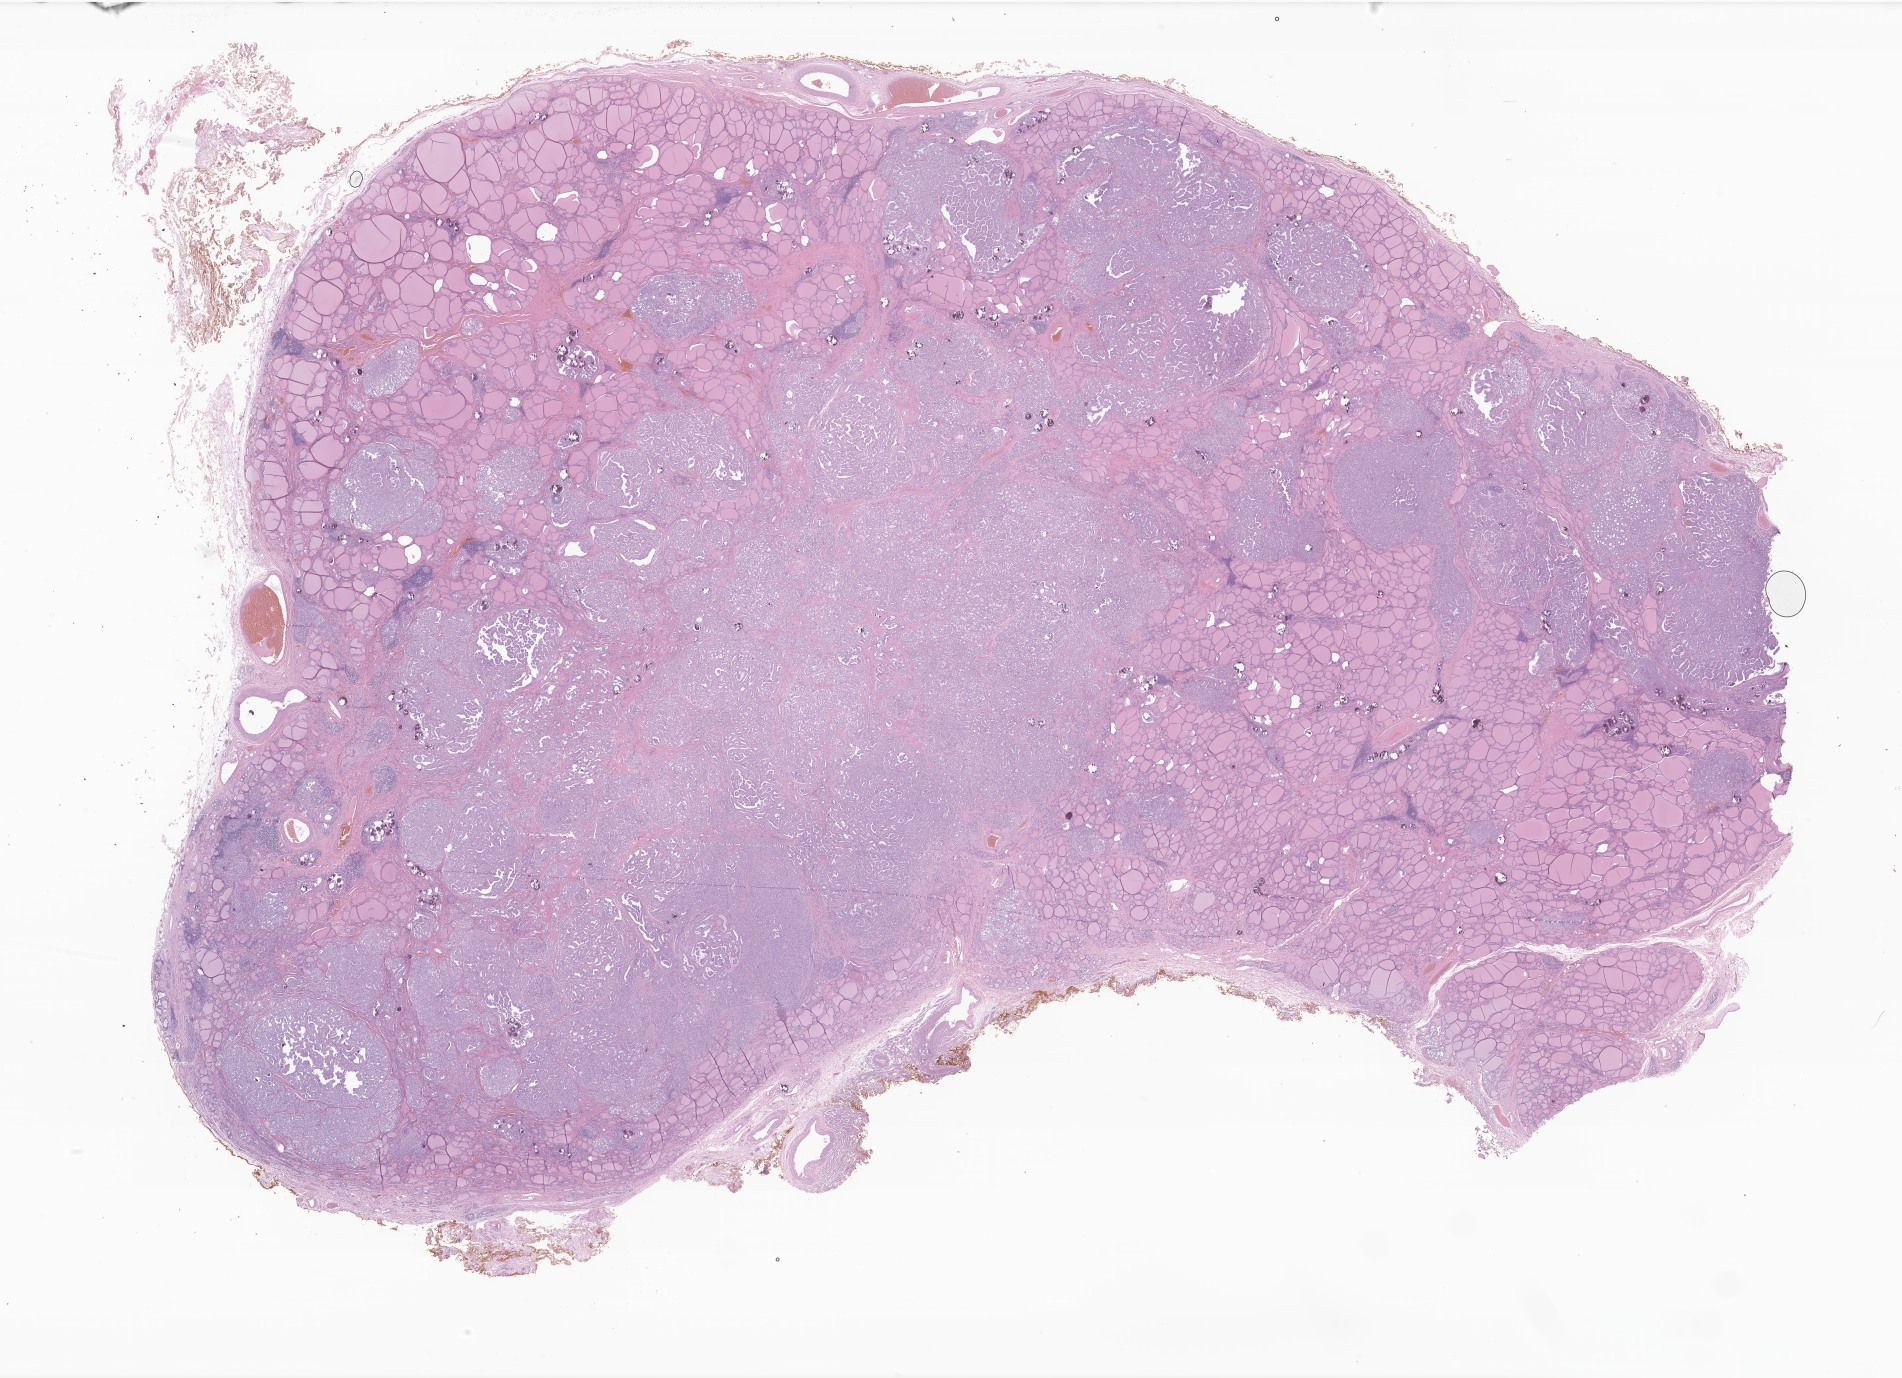
Digitized H&E-stained section of tumor tissue from the thyroid, a low-resolution overview of the entire scanned area, about 32.1 x 23.2 mm. FFPE section. Female patient, age 208 months (17 years 4 months).
Diagnosis (ICD-O-3 morphology term): Papillary carcinoma, NOS.